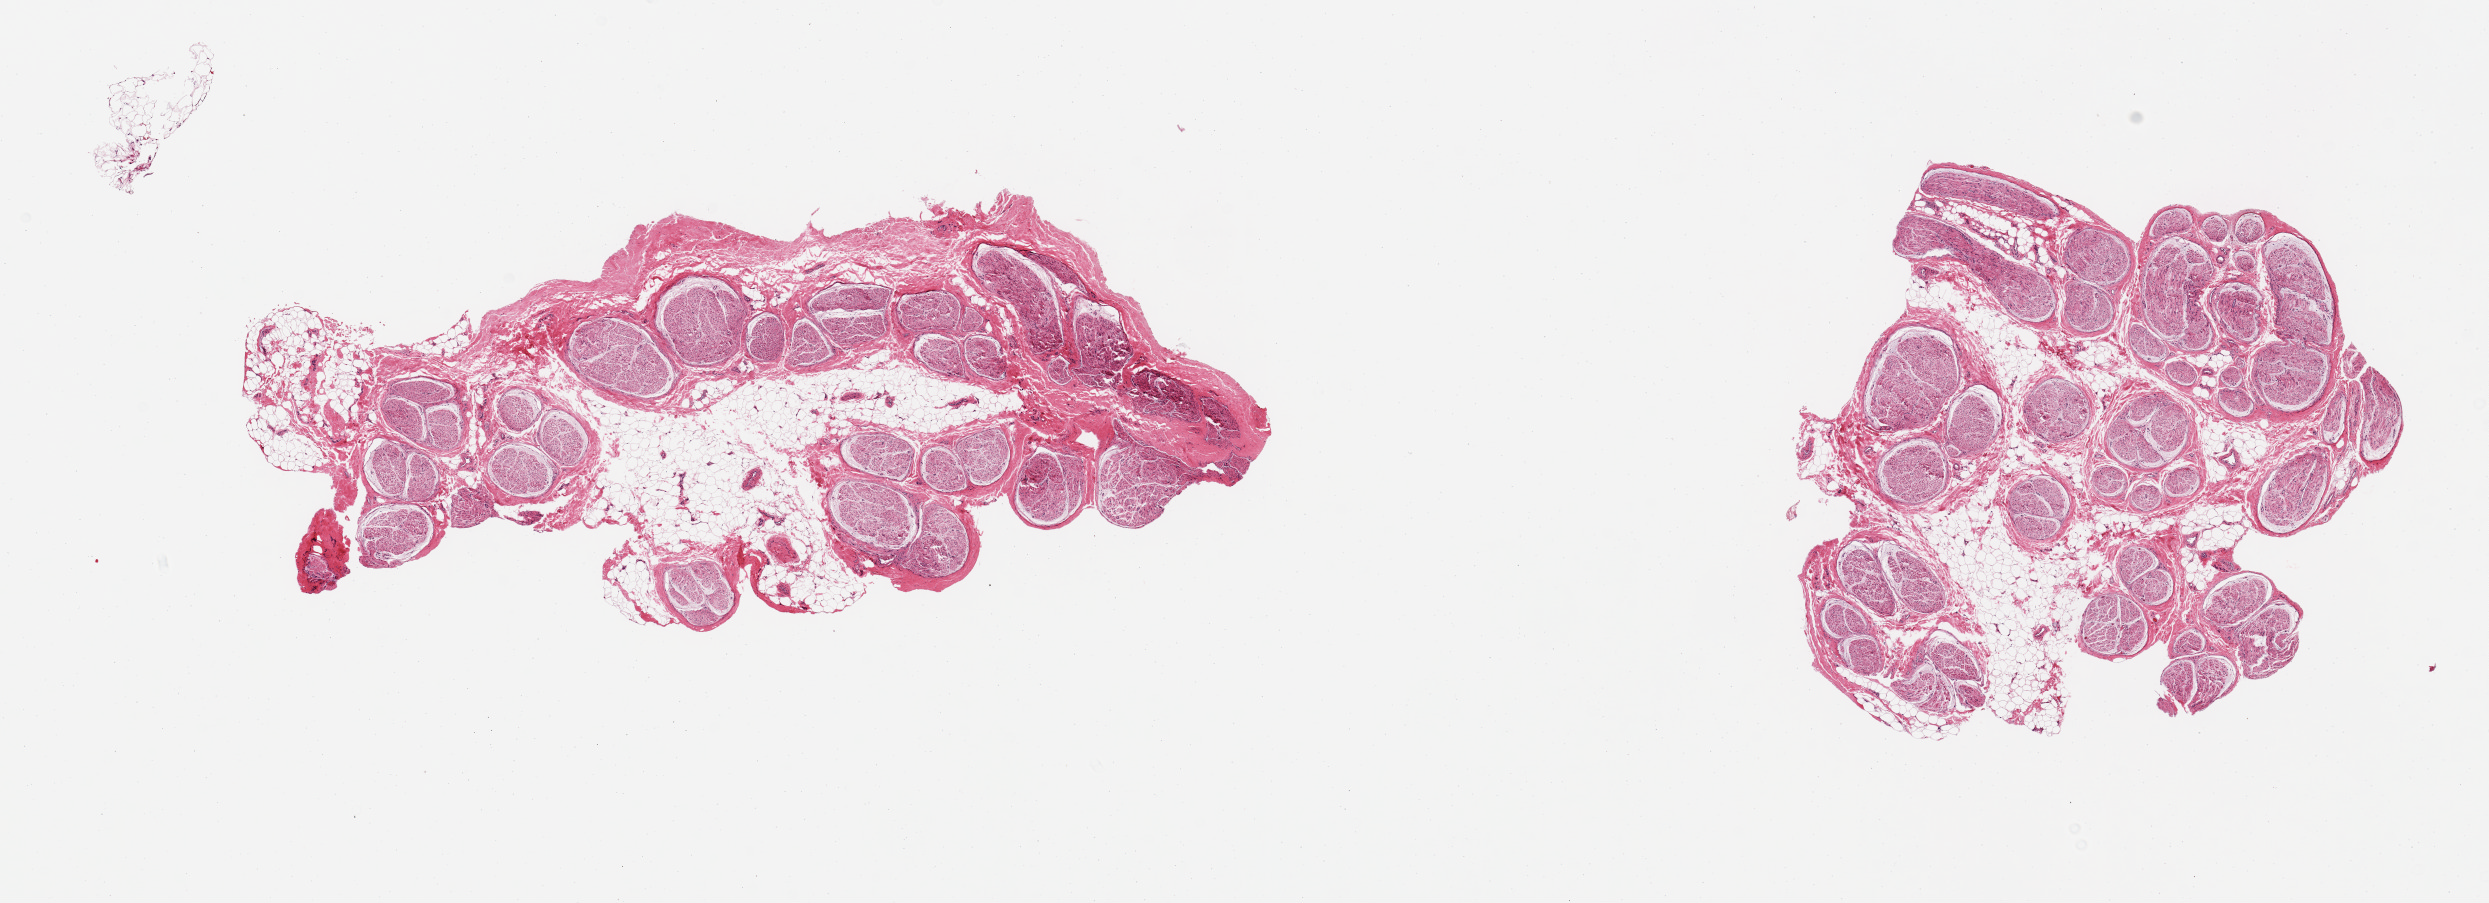
Whole-slide image, hematoxylin and eosin (H&E) stain, brightfield — low-resolution overview of the scanned area, about 19.7 x 7.1 mm; PAXgene-fixed paraffin-embedded (PFPE) section; target tissue: tibial nerve; donor tissue sample. Male donor.
Reviewer comment on this tissue sample: 2 pieces; one with 10% to 20% external fat and dense connective tissue and other with 10% to 20% internal fat.